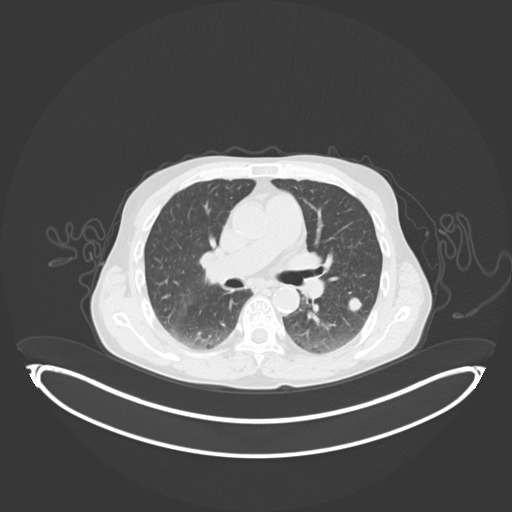
Chest CT, one axial slice; position 56 of 102 along the scan axis; lung window (W 1500 / L -600 HU); 3 mm slice thickness; 512 × 512 image matrix. Patient: male, 58 years. Case-level facts recorded for this patient, not image findings: clinical TNM (as recorded): T1c N0 M0.
Annotated regions visible in this slice (bounding box drawn by a radiologist):
- lung tumour (recorded histology: adenocarcinoma): bounding box [x1, y1, x2, y2] px = [346, 295, 363, 313]